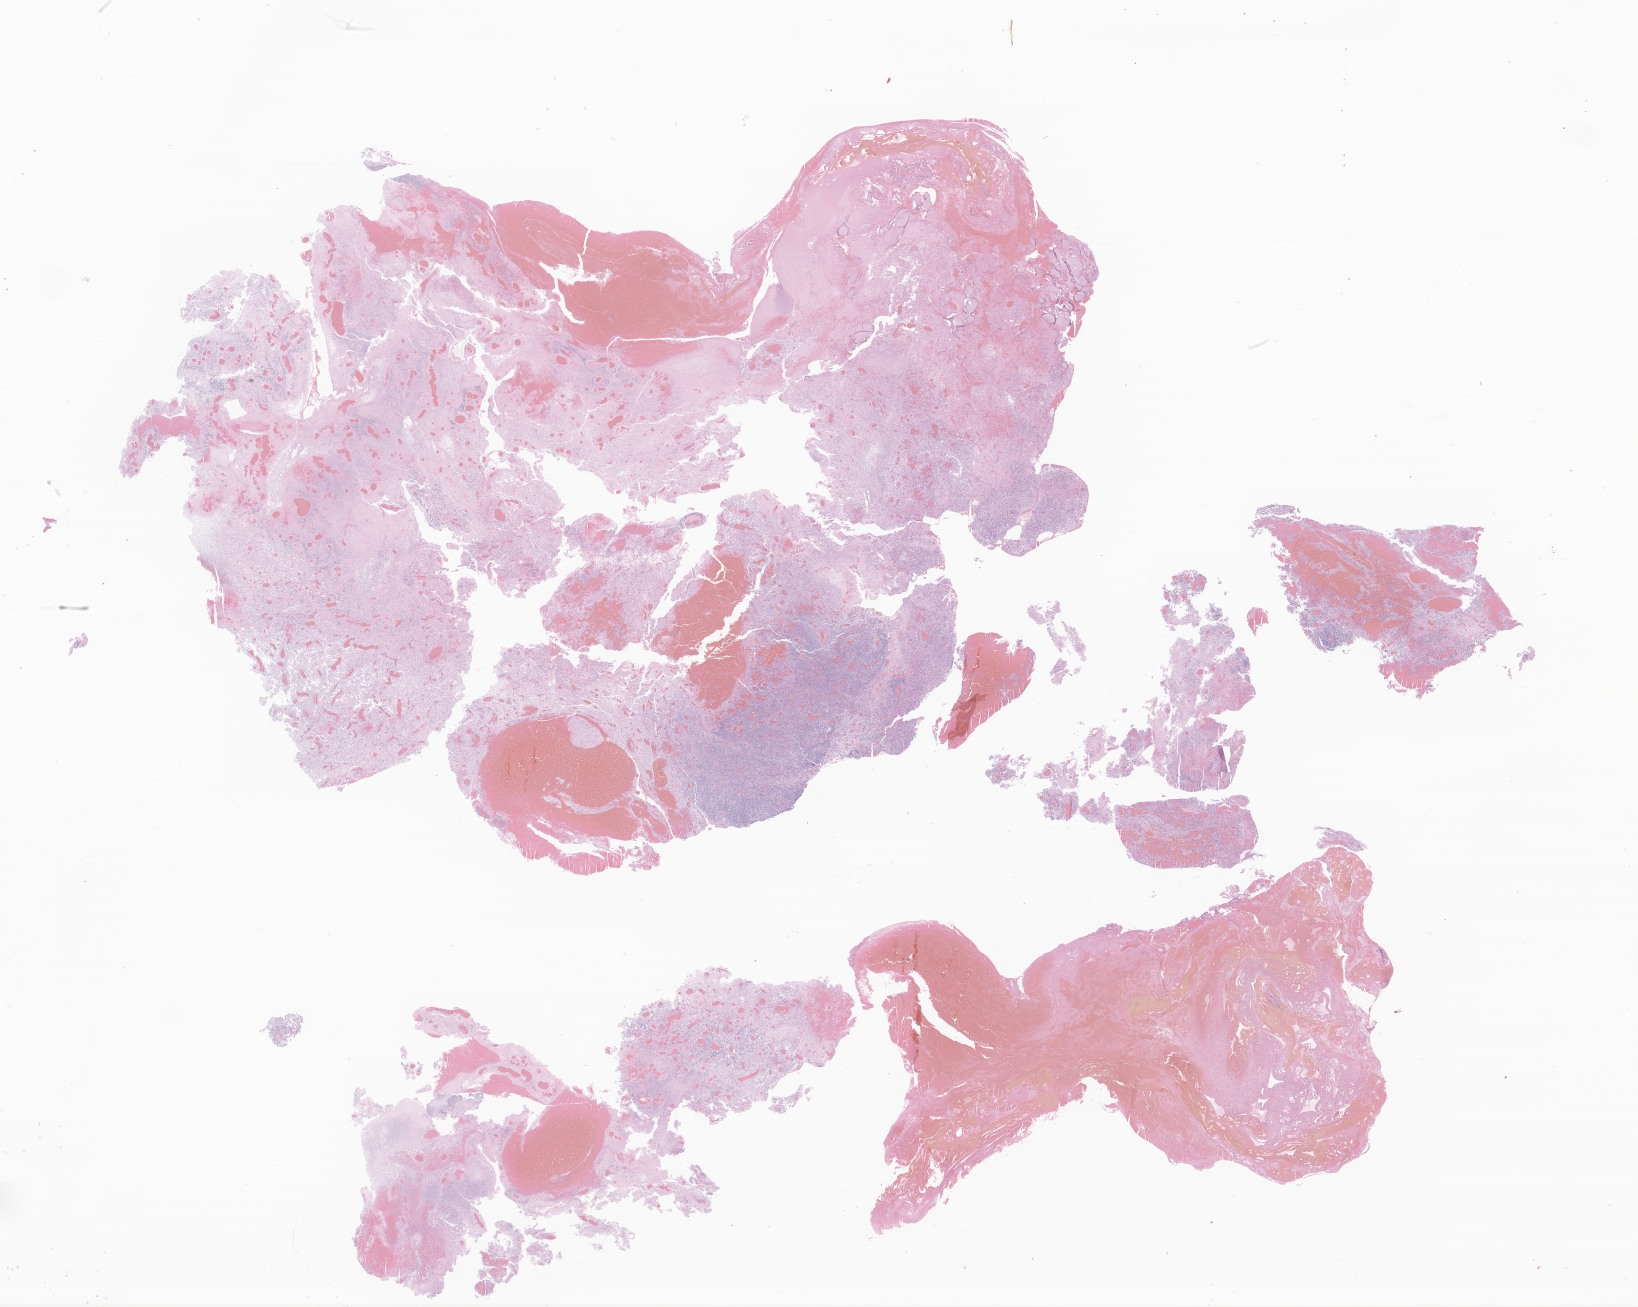
Whole-slide image, hematoxylin and eosin (H&E) stain of tumor tissue from the frontal lobe — shown as a low-resolution overview of the whole scanned area (about 27.6 x 22.0 mm), formalin-fixed paraffin-embedded section. Female patient, age 34 months (2 years 10 months).
Recorded diagnosis: Neoplasm, malignant.